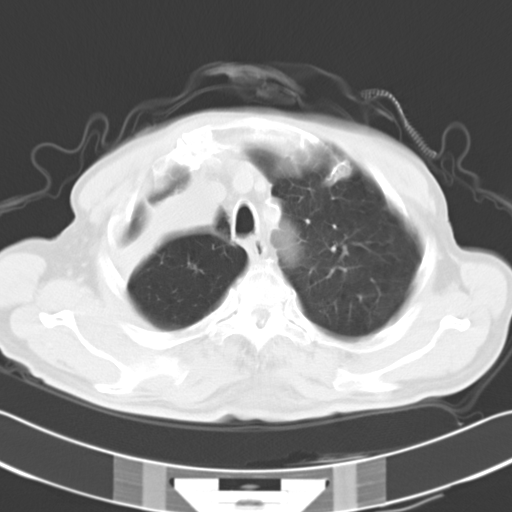
Chest CT, one axial slice; position 26 of 31 along the scan axis; reconstruction kernel B40f; 120 kVp; lung window (W 1500 / L -600 HU); 10 mm slice thickness; 512 × 512 image matrix, field of view 339 × 339 mm. Male patient, age 73 years. From the clinical record (not read from this slice): clinical TNM (as recorded): T2a N1 M0.
Annotated regions visible in this slice (rectangle marked by the reading radiologist):
- lung tumour (recorded histology: squamous cell carcinoma): bounding box <103,168,236,280> (left, top, right, bottom; pixels)